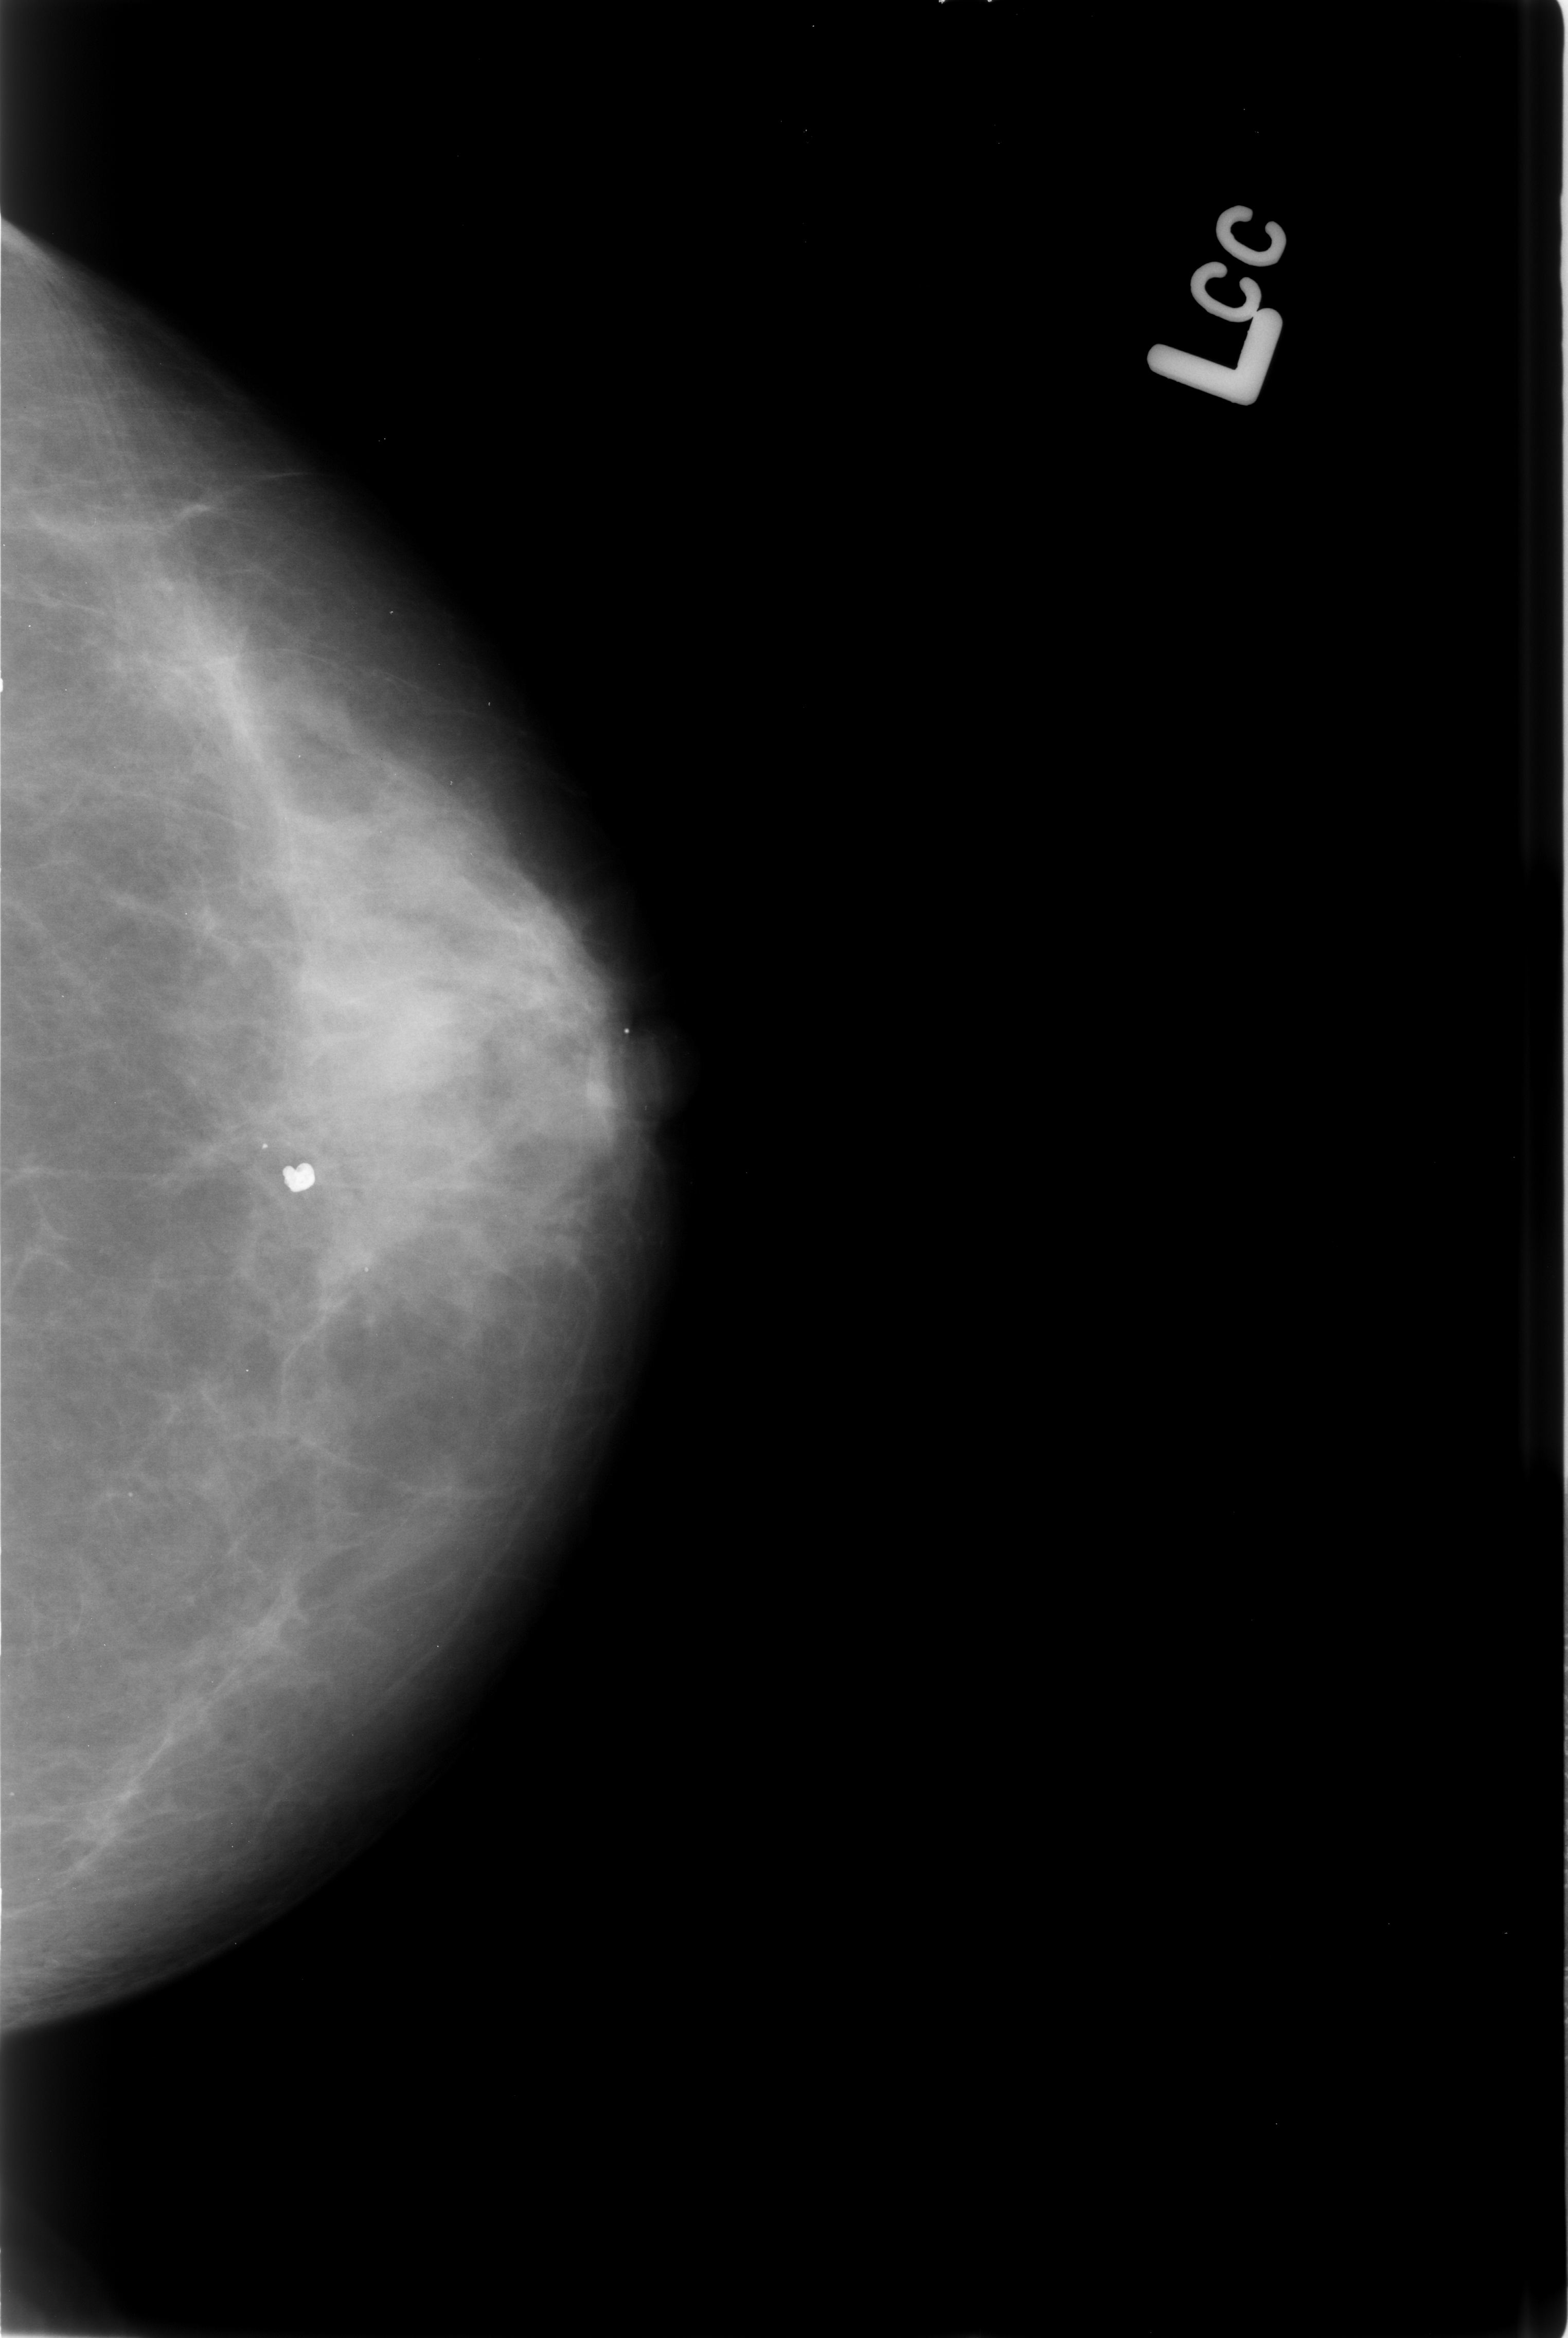
Mammogram (digitized film). Left breast. Craniocaudal (CC) view. BI-RADS breast density category 3 (scale 1–4). 1568 × 2338 image matrix.
Expert-marked regions of interest on this image (one box per marked abnormality):
- calcifications, morphology coarse; BI-RADS assessment category 2; benign; no additional work-up was recommended (outcome (as recorded, no biopsy): benign without callback): box from (x=255, y=1131) to (x=343, y=1232) px